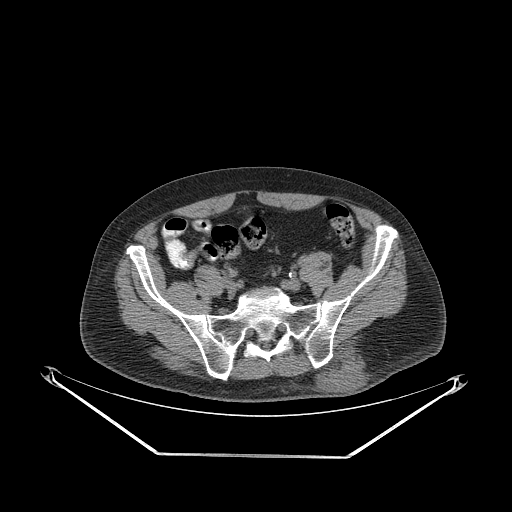
CT of an extremity soft-tissue mass (from a PET/CT study), one axial slice. Position 77 of 267 along the scan axis. 140 kVp. Soft-tissue window (W 400 / L 40 HU). 3.75 mm slice thickness. 512 × 512 image matrix. Male patient. From the clinical record (not read from this slice): histological type: leiomyosarcoma; grade: intermediate; site of the primary tumour: left pelvis.
Annotated regions visible in this slice (expert contour drawn on MRI and transferred to this co-registered scan by the dataset authors):
- gross tumour volume (mass): bounding box [x1, y1, x2, y2] px = [322, 356, 364, 396]